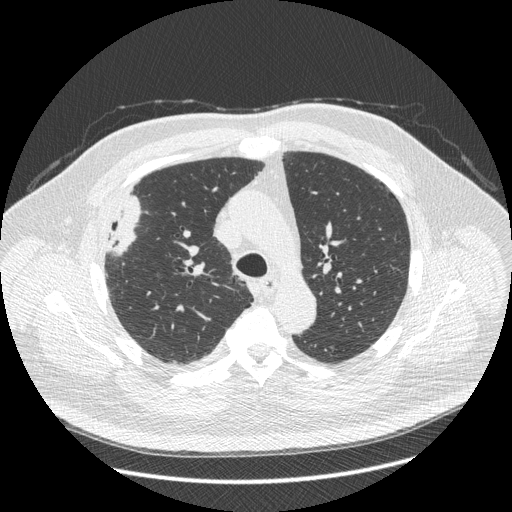
Low-dose screening chest CT, one axial slice. Slice 300 of 426 in the series (ordered by position). Reconstruction kernel STANDARD. 120 kVp. Lung window (W 1500 / L -600 HU). 512 × 512 image matrix, field of view 400 × 400 mm.
Structures marked on this image (manually delineated by an expert):
- lesion 1 (tumor, upper lobe of right lung): box from (x=105, y=196) to (x=141, y=254) px